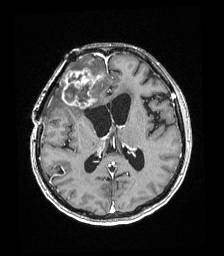
Brain MRI from a brain-tumour surgery series, one axial slice. Position 91 of 192 along the scan axis. T1-weighted post-contrast. 224 × 256 image matrix. Case-level facts recorded for this patient, not image findings: histopathology: Astrocytoma; WHO grade: 4; IDH mutation: yes.
Structures marked on this image (expert manual segmentation):
- tumour: box from (x=62, y=68) to (x=103, y=108) px